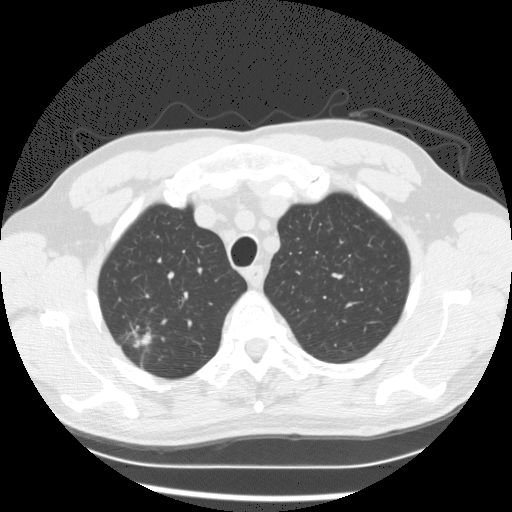
Low-dose screening chest CT, one axial slice; slice 108 of 132 in the series (ordered by position); reconstruction kernel STANDARD; 120 kVp; lung window (W 1500 / L -600 HU); 2.5 mm slice thickness; 512 × 512 image matrix, field of view 351 × 351 mm.
Annotated regions visible in this slice (manually delineated by an expert):
- lesion 1 (tumor, upper lobe of right lung): bounding box <140,332,151,346> (left, top, right, bottom; pixels)